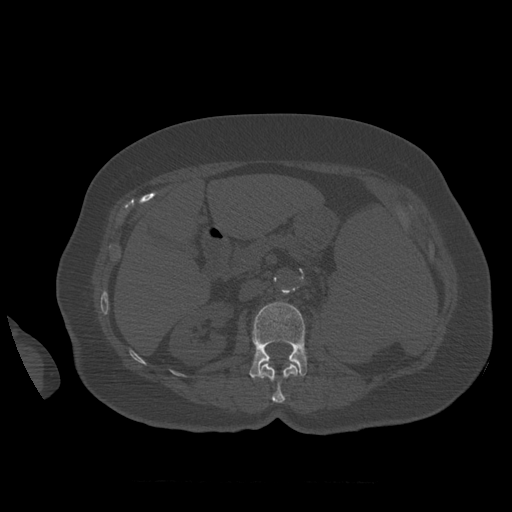
CT including the spine, one axial slice. Slice 262 of 399 in the series (ordered by position). Reconstruction kernel STANDARD. 120 kVp. Bone window (W 1800 / L 400 HU). 1.25 mm slice thickness. 512 × 512 image matrix, field of view 404 × 404 mm. Patient age 81 years. From the clinical record (not read from this slice): primary cancer: renal.
Structures marked on this image (semi-automatic segmentation, software-assisted and operator-edited):
- L1 vertebra: bounding box <259,363,299,403> (left, top, right, bottom; pixels)
- L2 vertebra: <250,302,307,380>